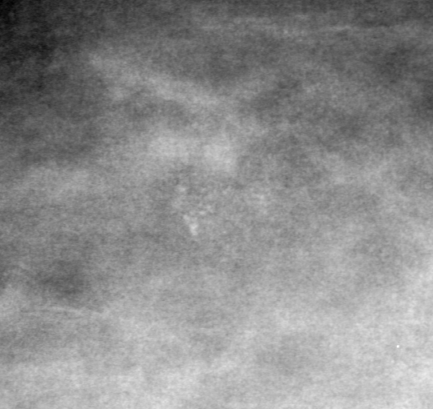
Cropped region of a digitized screen-film mammogram centred on a radiologist-marked abnormality; left breast; CC view; BI-RADS breast density category 3 (scale 1–4).
Finding: calcifications, morphology pleomorphic, distribution clustered; BI-RADS assessment category 4; subtlety rating 3 on a 1 (subtle) to 5 (obvious) scale; pathology (as recorded): malignant.